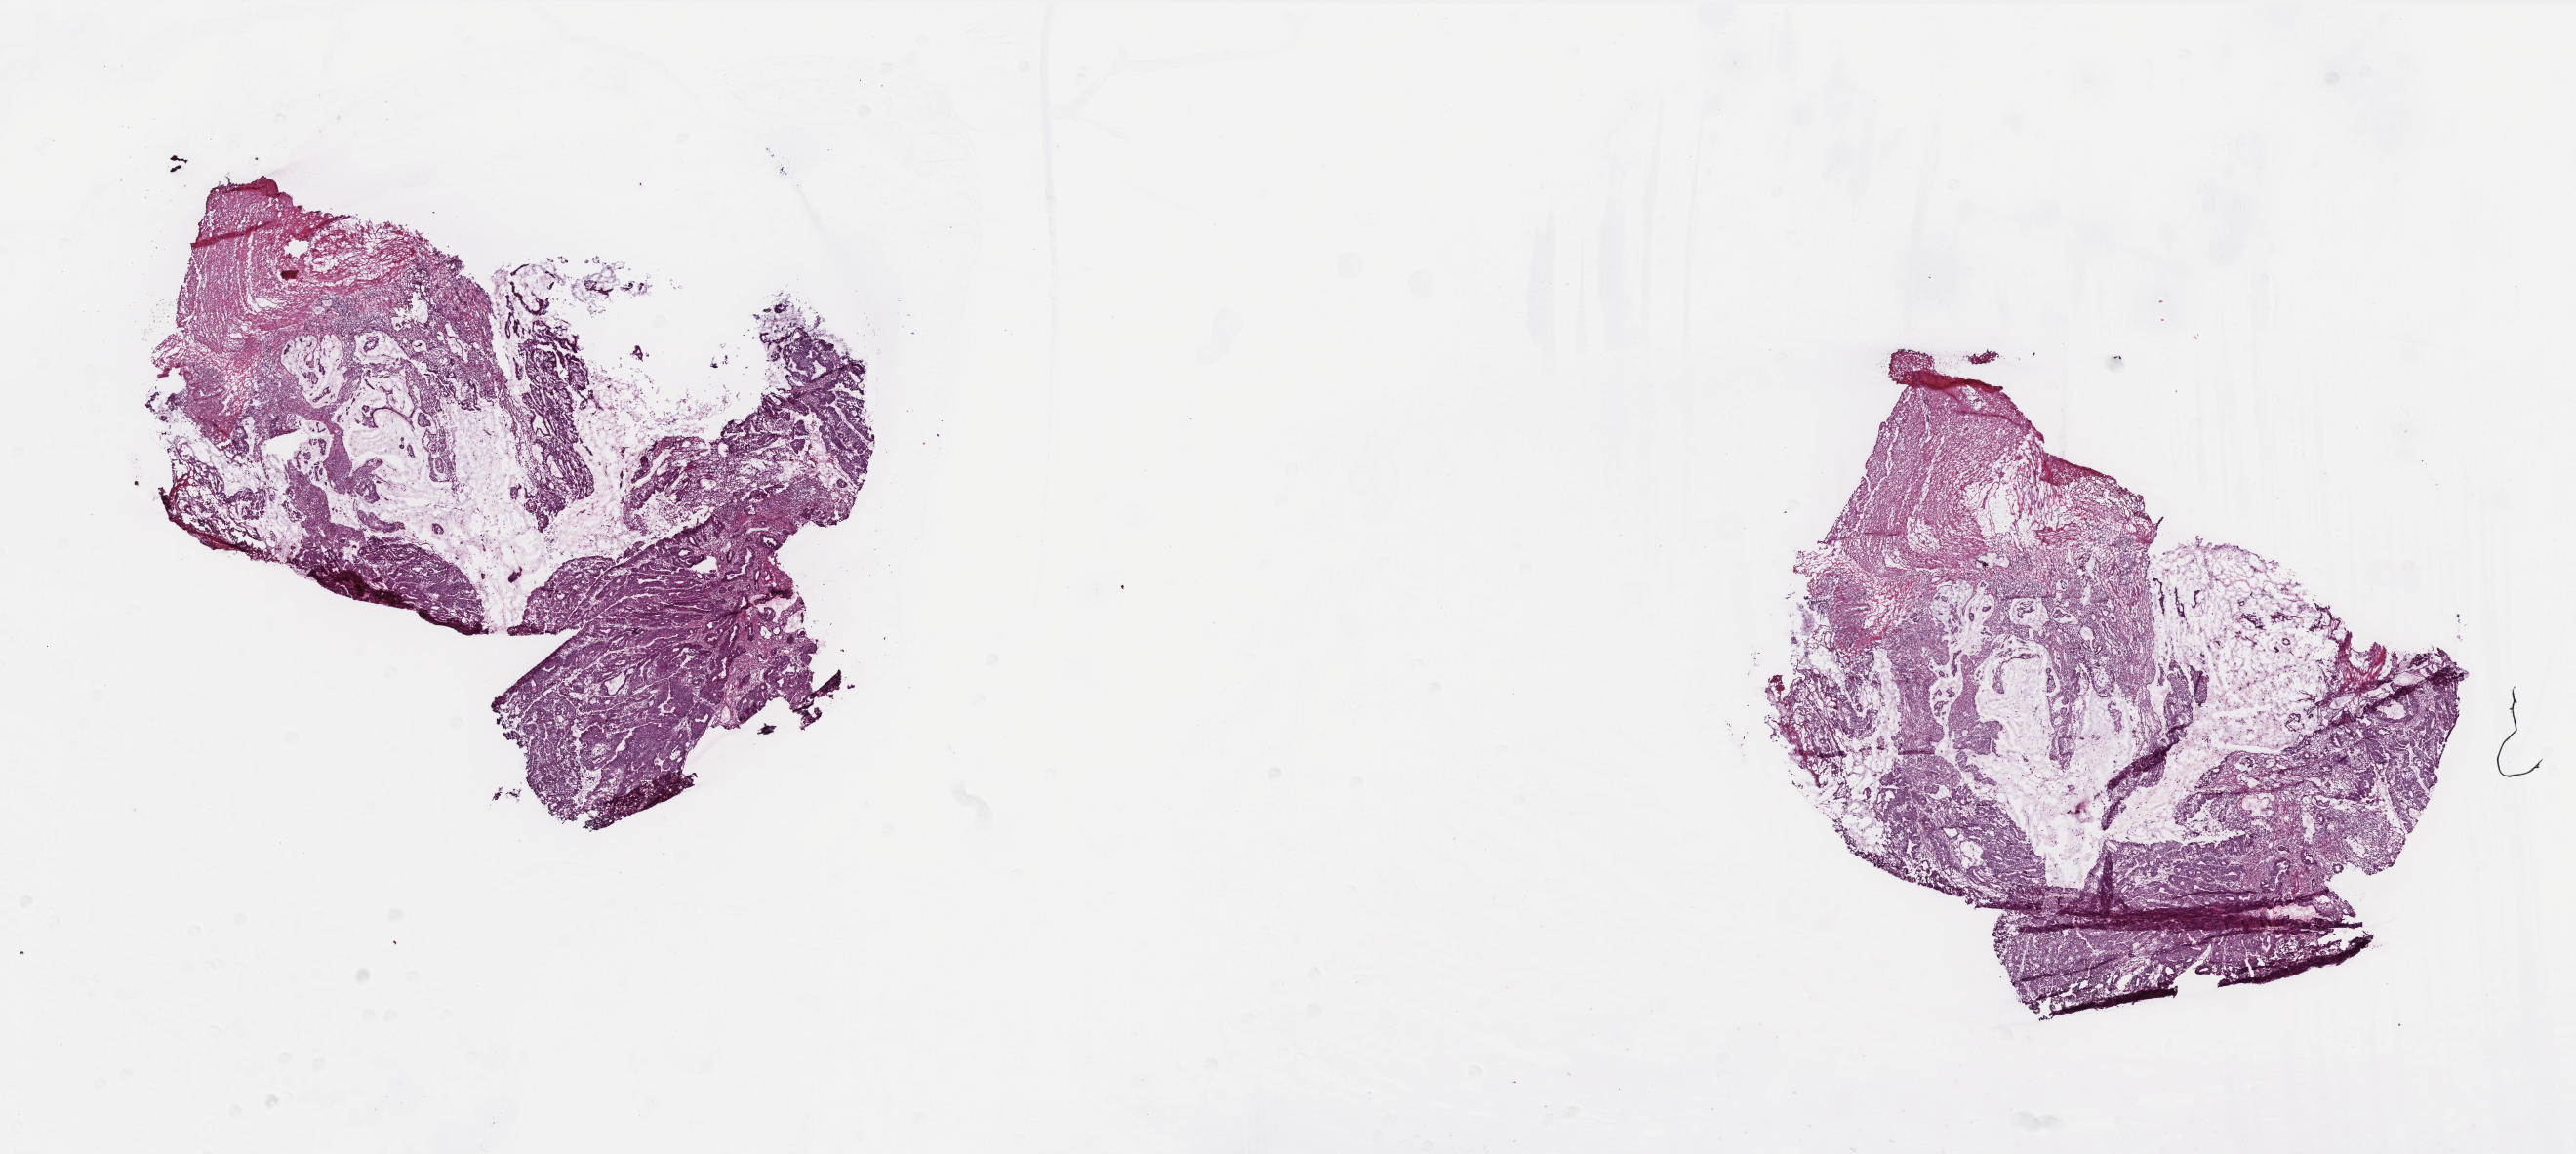
Whole-slide histology image, Hematoxylin and eosin (H&E) stained — low-resolution overview of the scanned area, about 21.2 x 9.5 mm; frozen section; primary tumour sample from the colon. Patient: female, age at initial diagnosis 47 years. Composition of this section per pathologist review: tumour cells 70%, tumour nuclei 75%, normal cells 0%, stromal cells 20%, necrosis 10%. Infiltration values recorded for this section: lymphocyte infiltration 15%, monocyte infiltration 3%, neutrophil infiltration 2%.
• diagnosis: Mucinous adenocarcinoma
• AJCC pathologic stage: IIIC